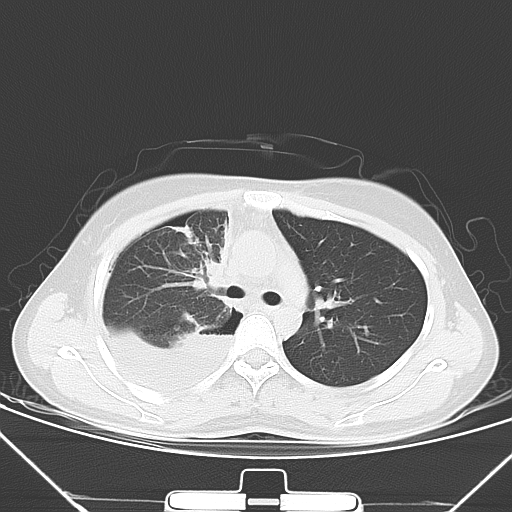
Chest CT, one axial slice. Slice 42 of 62 in the series (ordered by position). Lung window (W 1500 / L -600 HU). 5 mm slice thickness. 512 × 512 image matrix, field of view 343 × 343 mm. Female patient, age 28 years. From the clinical record (not read from this slice): clinical TNM (as recorded): T2 N0 M1a.
Structures marked on this image (rectangle marked by the reading radiologist):
- lung tumour (recorded histology: adenocarcinoma): bounding box [x1, y1, x2, y2] px = [197, 227, 230, 299]